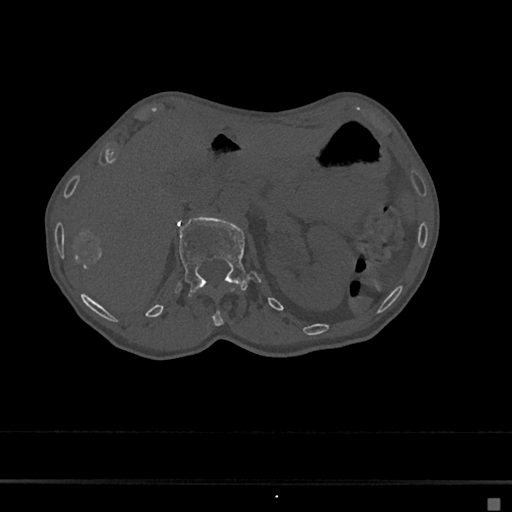
CT including the spine, one axial slice. Position 79 of 797 along the scan axis. Reconstruction kernel Br40s/3. 120 kVp. Bone window (W 1800 / L 400 HU). 512 × 512 image matrix, field of view 360 × 360 mm. Female patient, age 68 years. Case-level facts recorded for this patient, not image findings: primary cancer: renal.
Structures marked on this image (semi-automatic segmentation, software-assisted and operator-edited):
- L1 vertebra: bounding box [x1, y1, x2, y2] px = [176, 216, 261, 294]
- T12 vertebra: [206, 288, 240, 326]